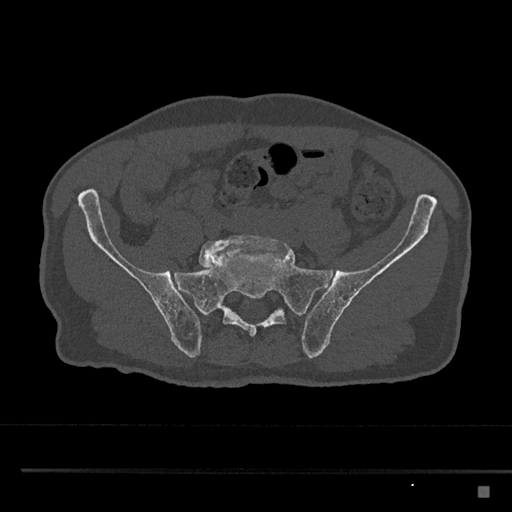
CT including the spine, one axial slice; position 531 of 797 along the scan axis; reconstruction kernel Br40s/3; bone window (W 1800 / L 400 HU); 0.5 mm slice thickness; 512 × 512 image matrix, field of view 391 × 391 mm. Male patient, age 59 years. From the clinical record (not read from this slice): primary cancer: prostate.
Annotated regions visible in this slice (semi-automatic segmentation, software-assisted and operator-edited):
- L5 vertebra: bounding box [x1, y1, x2, y2] px = [199, 234, 287, 268]